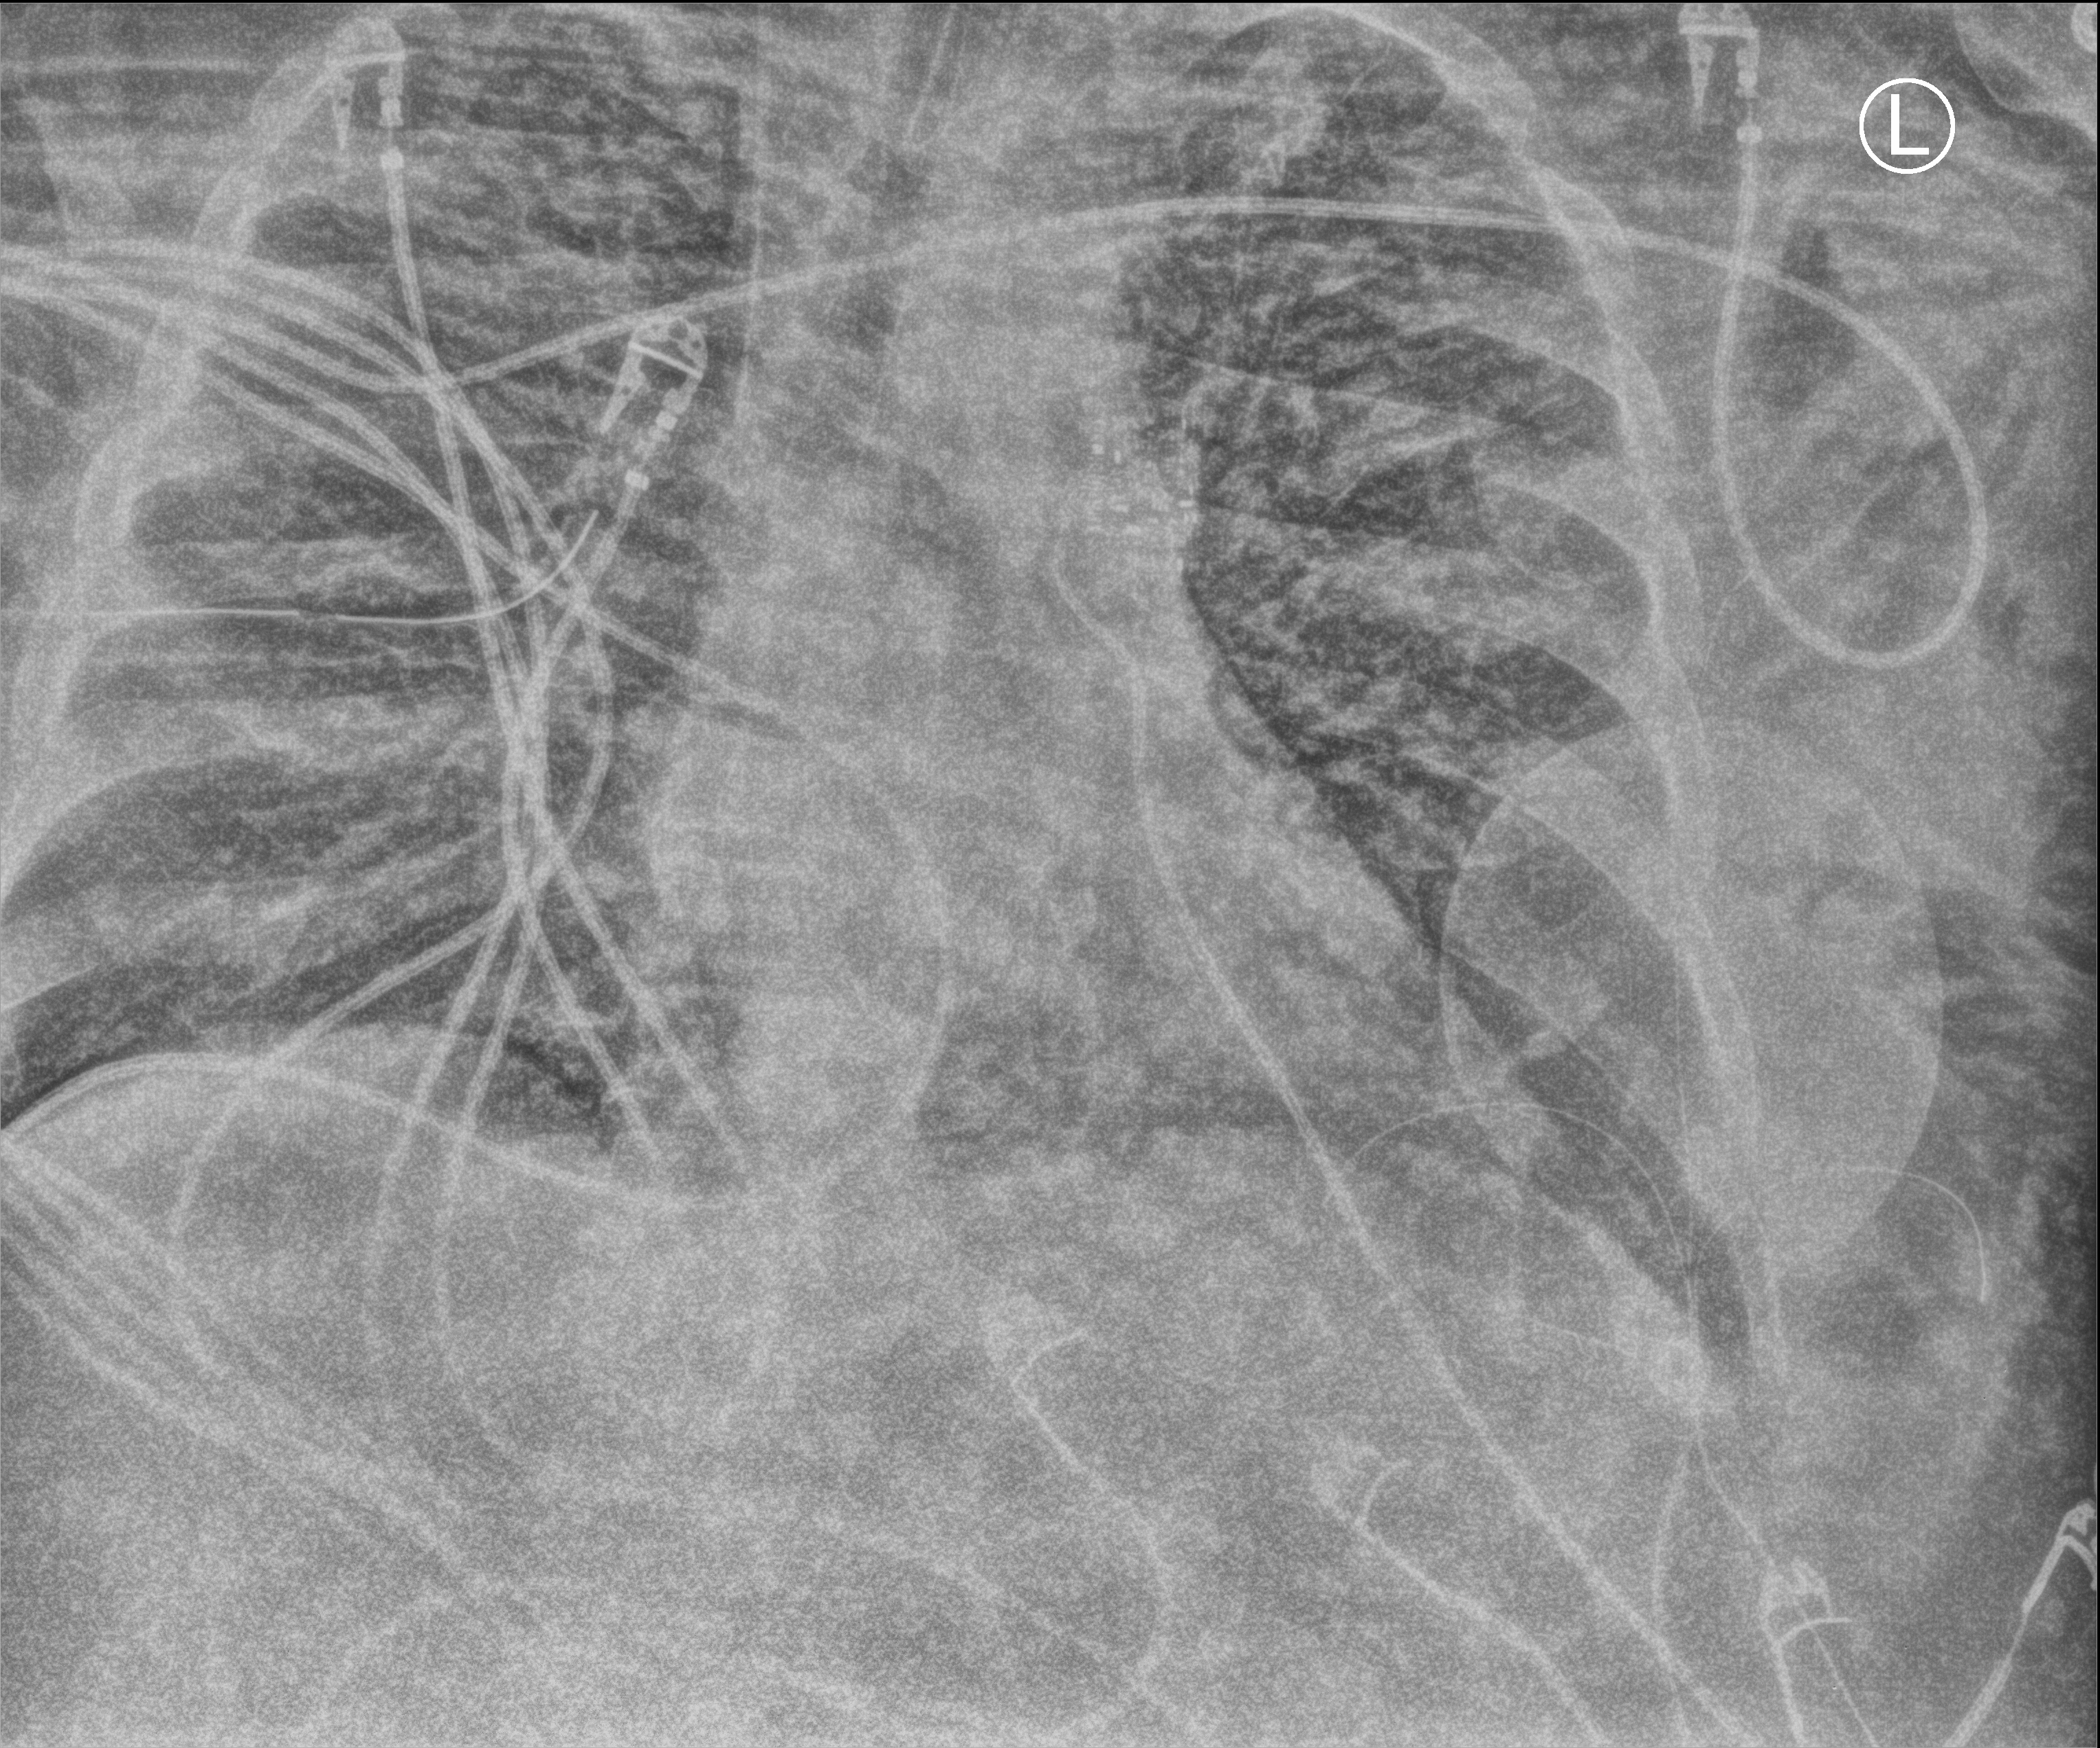
Chest X-ray (portable), anteroposterior (AP) projection. Patient hospitalised with COVID-19, aged 18–59 years.
Admission-level facts for this patient (not findings on this image; timing relative to this image not recorded):
- admitted to intensive care during this hospital stay: yes
- diabetes (admission record): yes